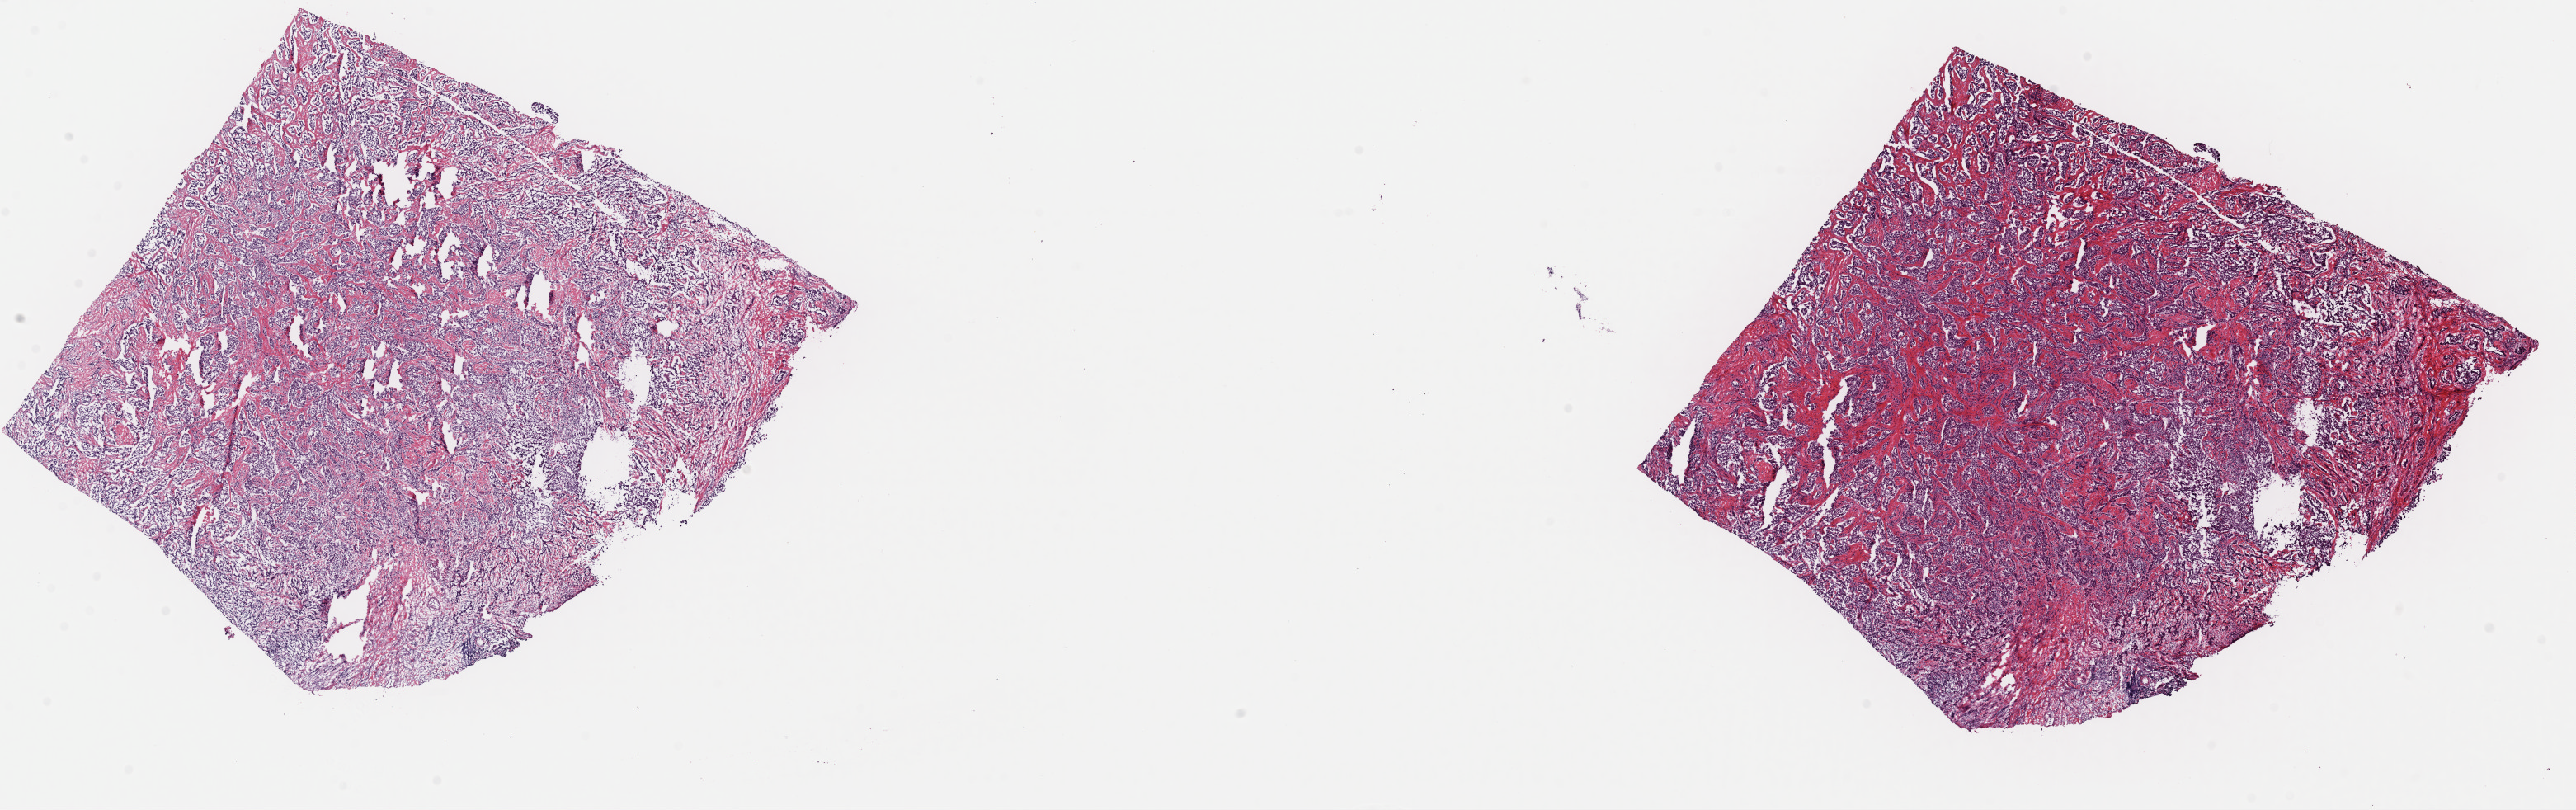
H&E-stained whole-slide image — low-resolution overview of the scanned area, about 24.7 x 7.8 mm. Frozen section from the top of the tissue portion. Sample: primary tumour, thyroid. Female patient; age at initial diagnosis 44 years. Pathologist review of this section (percent, as recorded): tumour cells 100%, tumour nuclei 80%, normal cells 0%, stromal cells 0%, necrosis 0%. Infiltration values recorded for this section: lymphocyte infiltration 0%, monocyte infiltration 0%, neutrophil infiltration 0%.
• lymph nodes positive (case pathology): 11 of 44 examined
• AJCC pathologic stage: I (7th edition)
• pathologic diagnosis: Papillary adenocarcinoma, NOS (thyroid gland)
• laterality: bilateral